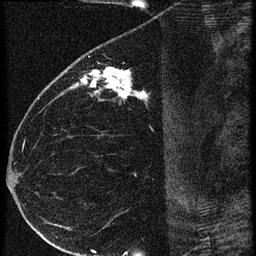
Breast MRI (dynamic contrast-enhanced), one sagittal slice. Position 31 of 60 along the scan axis. 3 images stored at this slice position (order not interpretable as contrast timing). 1.5 T. TE 4.2 ms, TR 20.4 ms. 1.5 mm slice thickness. 256 × 256 image matrix, field of view 180 × 180 mm. Female patient, age 35 years. From the clinical record (not read from this slice): setting: breast cancer imaged before/during neoadjuvant chemotherapy; receptor status: HR-positive, HER2-negative.
Structures marked on this image (semi-automatic segmentation, software-assisted and operator-edited):
- analysis volume of interest (the breast-tissue region the enhancement analysis was run in; not a lesion): bounding box (x1, y1, x2, y2) in pixels: (65, 60, 169, 119)
- tumour enhancement mask (voxels above the 90 % enhancement threshold inside the analysis volume of interest): (71, 68, 146, 99)